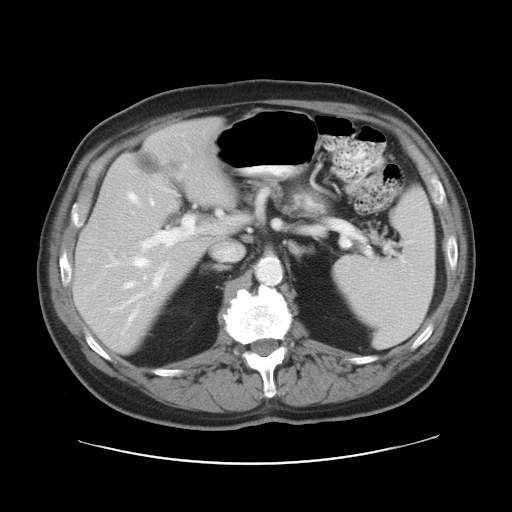
Contrast-enhanced abdominal CT, one axial slice; position 17 of 28 along the scan axis; intravenous contrast given; soft-tissue window (W 400 / L 40 HU); 7.5 mm slice thickness; 512 × 512 image matrix, field of view 402 × 402 mm. Male patient, age 74 years. Case-level facts recorded for this patient, not image findings: diagnosis: colorectal cancer liver metastases, imaged before liver resection; multiple liver metastases: no; largest metastasis: 5 cm.
Structures marked on this image (expert manual segmentation):
- hepatic veins: bounding box (x1, y1, x2, y2) in pixels: (118, 192, 169, 323)
- liver: (74, 120, 233, 350)
- planned liver remnant (the part of the liver to remain after resection): (74, 174, 200, 350)
- portal vein (with intrahepatic branches): (142, 216, 197, 248)
- liver metastasis: (137, 154, 165, 174)